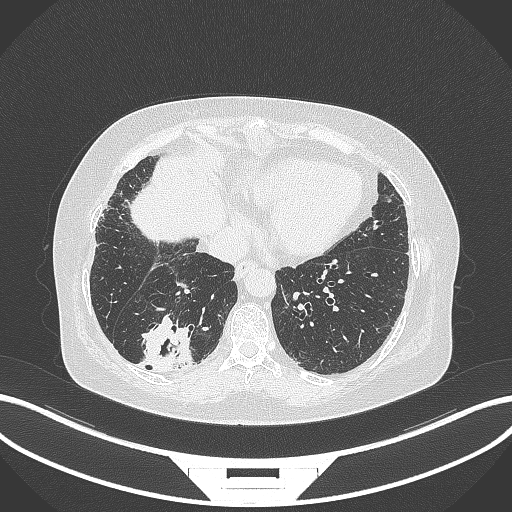
Chest CT, one axial slice. Slice 59 of 296 in the series (ordered by position). Reconstruction kernel B70f. 120 kVp. Lung window (W 1500 / L -600 HU). 1 mm slice thickness. 512 × 512 image matrix, field of view 400 × 400 mm. Patient: female, 65 years. From the clinical record (not read from this slice): clinical TNM (as recorded): T2b N1 M0; histopathological grade: G1.
Annotated regions visible in this slice (rectangle marked by the reading radiologist):
- lung tumour (recorded histology: adenocarcinoma): bounding box (x1, y1, x2, y2) in pixels: (138, 312, 201, 376)